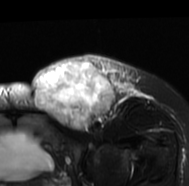
MRI of an extremity soft-tissue mass, one axial slice. Slice 48 of 77 in the series (ordered by position). T2-weighted fat-saturated. MR volume resampled by the dataset authors to the PET/CT grid (not the native acquisition matrix). 3.27 mm slice thickness. 189 × 186 image matrix. Female patient. Case-level facts recorded for this patient, not image findings: histological type: leiomyosarcoma; grade: high; site of the primary tumour: groin.
Annotated regions visible in this slice (expert contour drawn on MRI and transferred to this co-registered scan by the dataset authors):
- gross tumour volume including surrounding oedema: bounding box (x1, y1, x2, y2) in pixels: (29, 54, 151, 131)
- gross tumour volume (mass): (31, 56, 114, 130)